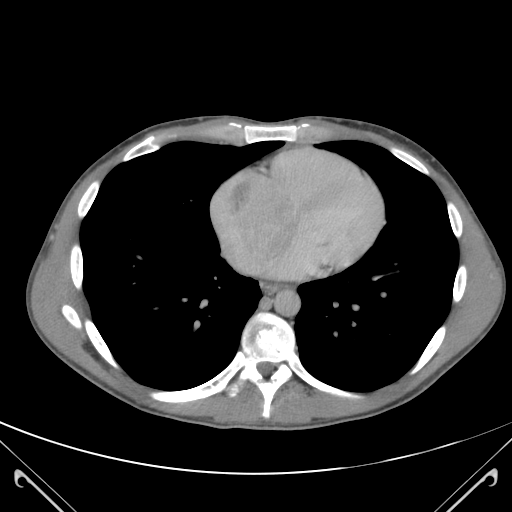
Contrast-enhanced abdominal CT (liver protocol), one axial slice. Slice 118 of 118 in the series (ordered by position). 120 kVp. Soft-tissue window (W 400 / L 40 HU). 3 mm slice thickness. 512 × 512 image matrix. From the clinical record (not read from this slice): diagnosis: hepatocellular carcinoma (patient treated with transarterial chemoembolisation; whether this scan precedes or follows treatment is not stated here); TNM stage (as recorded): Stage-IIIB; Child-Pugh class: A; tumour nodularity: uninodular.
Structures marked on this image (semi-automatic segmentation, software-assisted and operator-edited):
- abdominal aorta: bounding box [x1, y1, x2, y2] px = [270, 288, 299, 316]